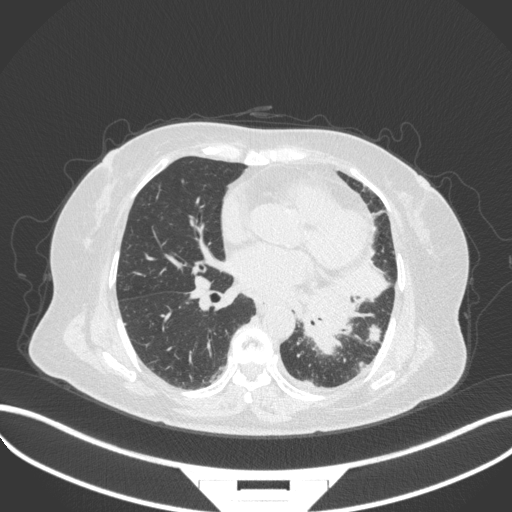
Chest CT, one axial slice. Lung window (W 1500 / L -600 HU). 512 × 512 image matrix, field of view 400 × 400 mm. Female patient, age 69 years. From the clinical record (not read from this slice): clinical TNM (as recorded): T2b N3 M1.
Structures marked on this image (rectangle marked by the reading radiologist):
- lung tumour (recorded histology: adenocarcinoma): bounding box <297,282,359,362> (left, top, right, bottom; pixels)